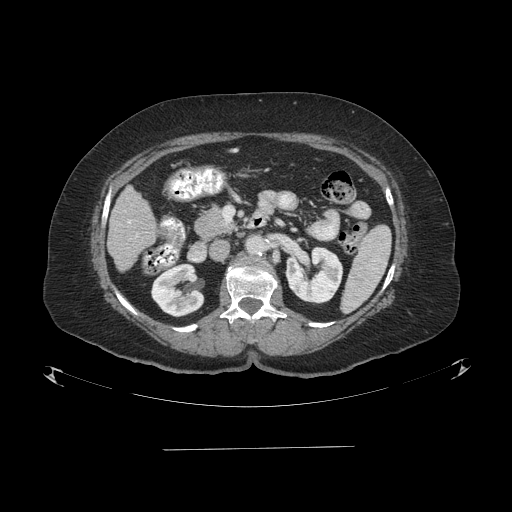
Contrast-enhanced abdominal CT (liver protocol), one axial slice. Slice 31 of 103 in the series (ordered by position). 120 kVp. One of 2 acquisitions stored at this slice position. Soft-tissue window (W 400 / L 40 HU). 2.5 mm slice thickness. 512 × 512 image matrix, field of view 500 × 500 mm. Case-level facts recorded for this patient, not image findings: diagnosis: hepatocellular carcinoma (patient treated with transarterial chemoembolisation; whether this scan precedes or follows treatment is not stated here); TNM stage (as recorded): Stage-IIIA; Child-Pugh class: A; tumour differentiation: poorly differentiated; tumour size: 5.2 cm.
Outlined on this slice (semi-automatic segmentation, software-assisted and operator-edited):
- liver parenchyma outside the tumour (the mass and vessels are separate outlines, so this box may not span the whole liver): bounding box [x1, y1, x2, y2] px = [108, 186, 156, 270]
- liver vessels: [128, 221, 131, 223]